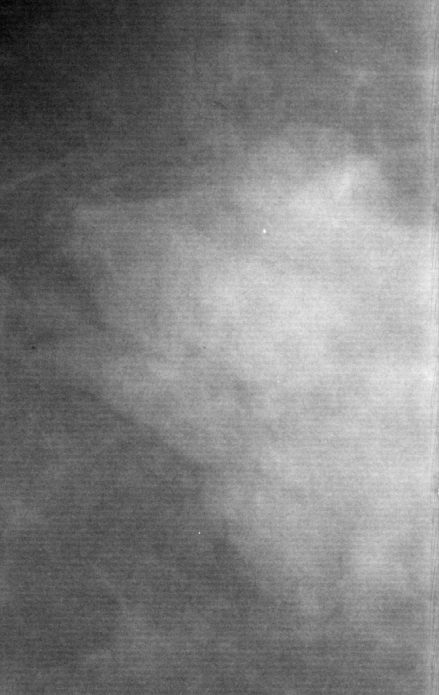
Cropped region of a digitized screen-film mammogram centred on a radiologist-marked abnormality, right breast, CC view, BI-RADS breast density category 1 (scale 1–4).
Finding: mass, shape lobulated, margins microlobulated; BI-RADS assessment category 5; subtlety rating 5 on a 1 (subtle) to 5 (obvious) scale; pathology (as recorded): malignant.